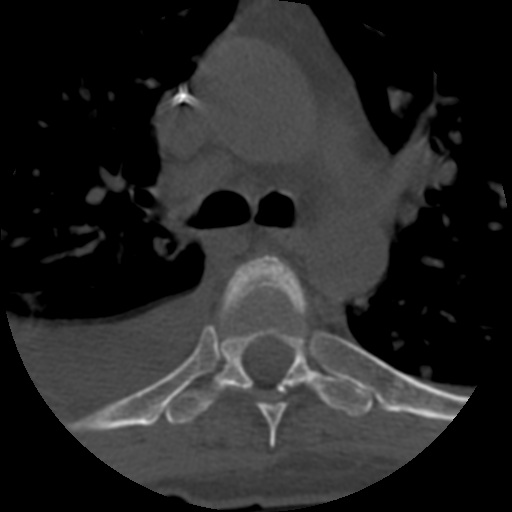
CT including the spine, one axial slice; position 444 of 708 along the scan axis; reconstruction kernel STANDARD; 120 kVp; one of 3 acquisitions stored at this slice position; bone window (W 1800 / L 400 HU); 1.25 mm slice thickness; 512 × 512 image matrix, field of view 160 × 160 mm. Patient age 55 years. From the clinical record (not read from this slice): primary cancer: colon; vertebrae with lytic lesions (as recorded): T12, L1, L5.
Outlined on this slice (semi-automatically segmented with operator editing):
- T5 vertebra: bounding box [x1, y1, x2, y2] px = [222, 254, 305, 448]
- T6 vertebra: [164, 278, 373, 426]